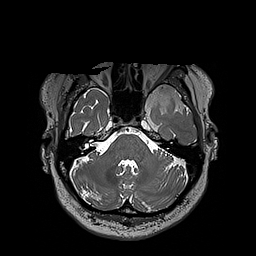
Brain MRI from a brain-tumour surgery series, one axial slice; slice 148 of 192 in the series (ordered by position); 1 mm slice thickness; 256 × 256 image matrix, field of view 250 × 250 mm. From the clinical record (not read from this slice): histopathology: Oligodendroglioma; WHO grade: 3; IDH mutation: yes.
Outlined on this slice (expert manual segmentation):
- tumour: bounding box (x1, y1, x2, y2) in pixels: (124, 84, 197, 112)